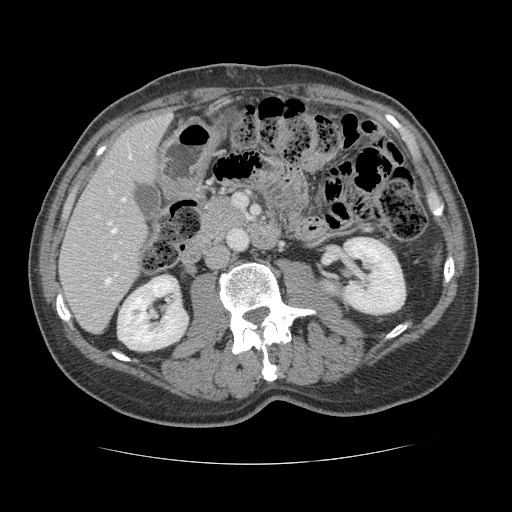
Contrast-enhanced abdominal CT, one axial slice. Position 54 of 134 along the scan axis. Reconstruction kernel STANDARD. Soft-tissue window (W 400 / L 40 HU). 2.5 mm slice thickness. 512 × 512 image matrix, field of view 377 × 377 mm. Male patient, age 68 years. Case-level facts recorded for this patient, not image findings: diagnosis: colorectal cancer liver metastases, imaged before liver resection; multiple liver metastases: yes; largest metastasis: 2.2 cm; chemotherapy before resection: no.
Annotated regions visible in this slice (manually delineated by an expert):
- hepatic veins: box from (x=108, y=154) to (x=131, y=233) px
- liver: (x=60, y=115)–(x=169, y=332)
- planned liver remnant (the part of the liver to remain after resection): (x=60, y=115)–(x=169, y=332)
- portal vein (with intrahepatic branches): (x=105, y=255)–(x=117, y=284)